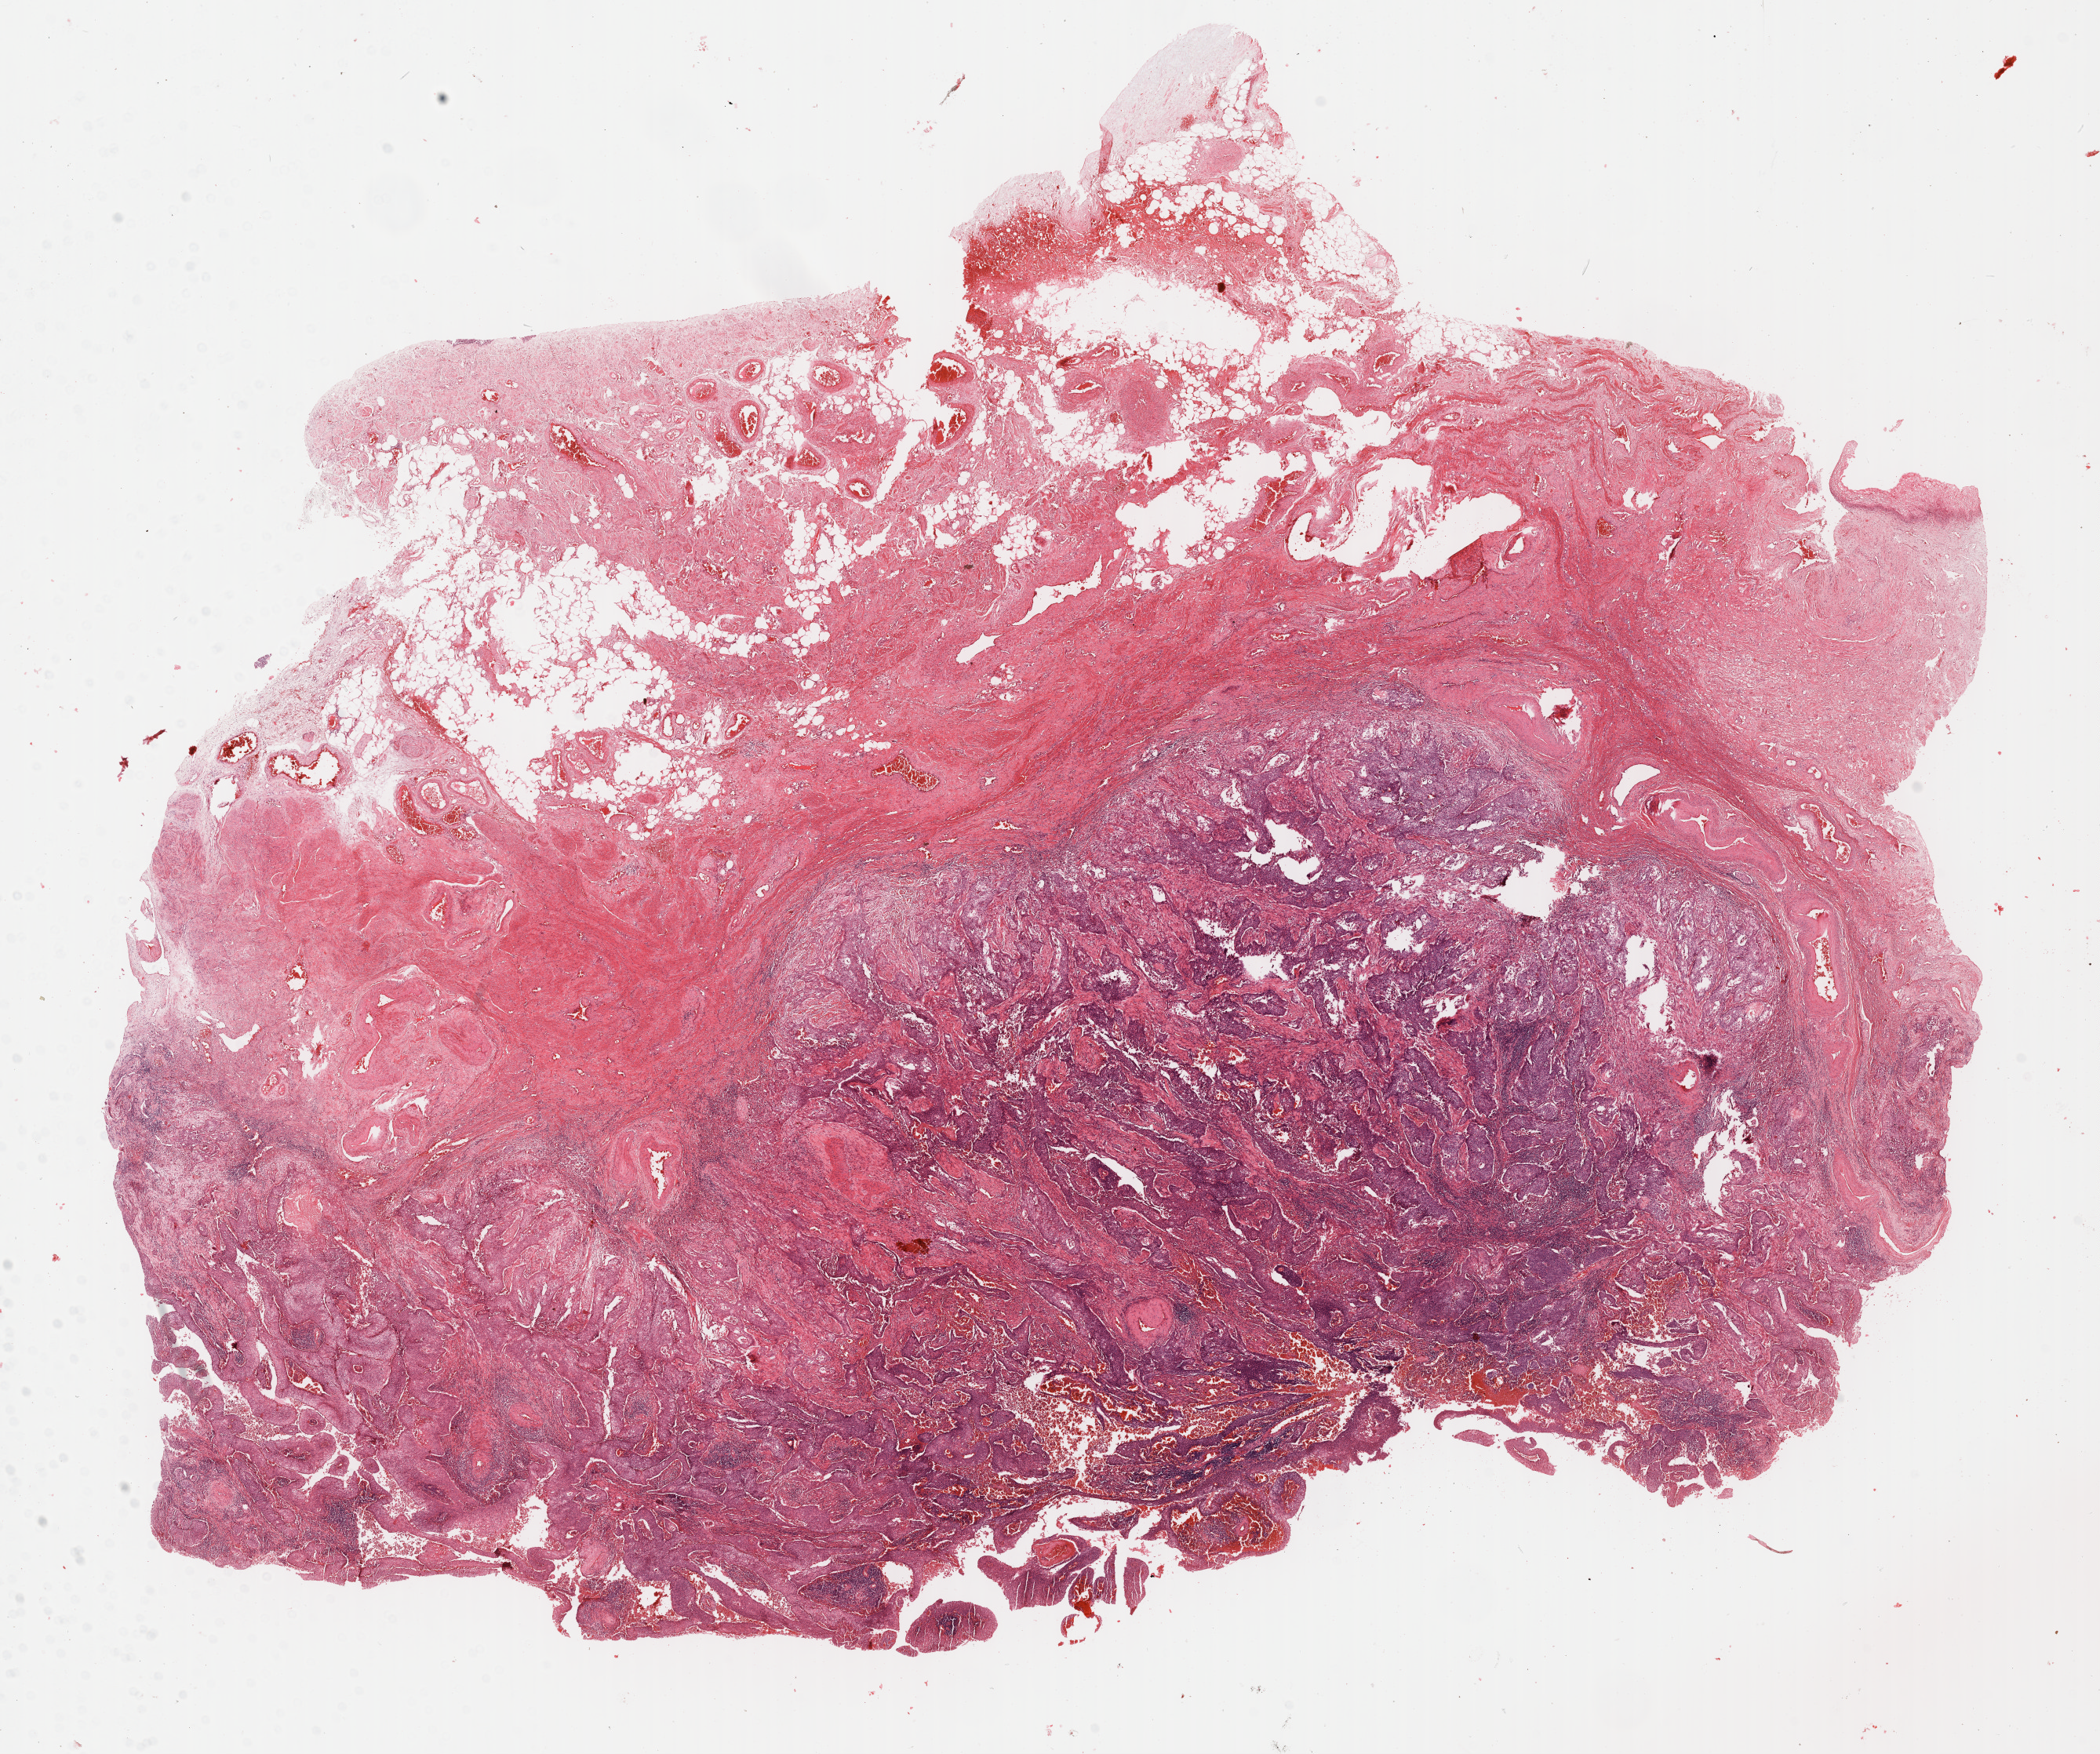
Digitized Hematoxylin and eosin (H&E) stained tissue section (whole slide) — whole scanned area (about 21.0 x 17.6 mm) shown as a low-resolution overview; formalin-fixed paraffin-embedded (FFPE) diagnostic section; primary tumour sample from the cervix. Female patient; age at initial diagnosis 52 years. Histologic grade: G1 (well differentiated).
FIGO stage: IA. Pathologic diagnosis: Squamous cell carcinoma, keratinizing, NOS (cervix uteri).